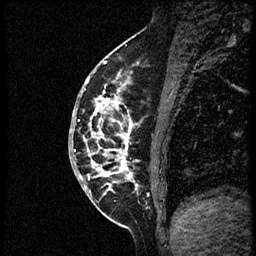
Breast MRI (dynamic contrast-enhanced), one sagittal slice; position 23 of 56 along the scan axis; dynamic contrast-enhanced study with each time point stored as its own series, time point 2 of 3 at this slice position (early post-contrast, ordered by acquisition time); 1.5 T; TE 4.2 ms, TR 21.3 ms; 2 mm slice thickness; 256 × 256 image matrix, field of view 200 × 200 mm. Female patient, age 41 years. Case-level facts recorded for this patient, not image findings: setting: breast cancer imaged before/during neoadjuvant chemotherapy; receptor status: HER2-positive.
Outlined on this slice (semi-automatically segmented with operator editing):
- analysis volume of interest (the breast-tissue region the enhancement analysis was run in; not a lesion): box from (x=70, y=73) to (x=177, y=205) px
- tumour enhancement mask (voxels above the 100 % enhancement threshold inside the analysis volume of interest): (x=74, y=74)–(x=133, y=188)